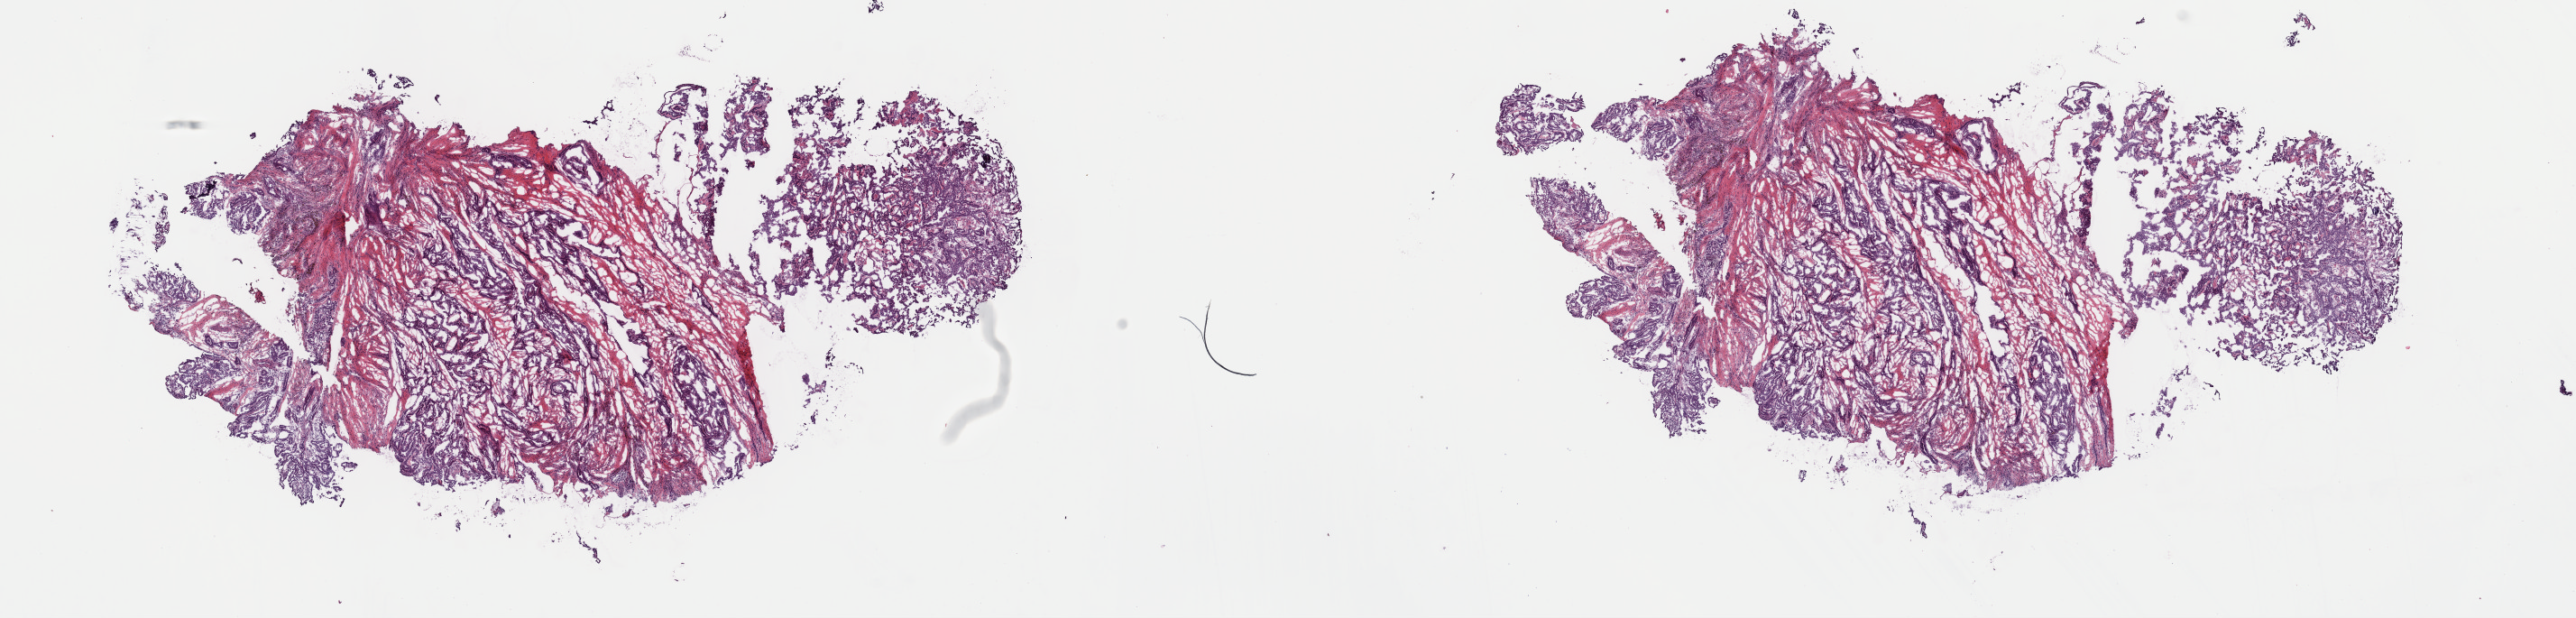
Hematoxylin and eosin (H&E) stained whole-slide image, whole scanned area (about 22.6 x 5.4 mm) shown as a low-resolution overview. Frozen section from the top of the tissue portion. Sample: primary tumour, thyroid. Female, age 33 years at initial diagnosis. Pathologist review of this section (percent, as recorded): tumour cells 70%, tumour nuclei 80%, normal cells 0%, stromal cells 30%, necrosis 0%. Infiltration values recorded for this section: lymphocyte infiltration 2%, monocyte infiltration 0%, neutrophil infiltration 0%.
- lymph nodes positive (case pathology): 13 of 43 examined
- diagnosis: Papillary adenocarcinoma, NOS (thyroid gland)
- AJCC pathologic stage: I (7th edition)